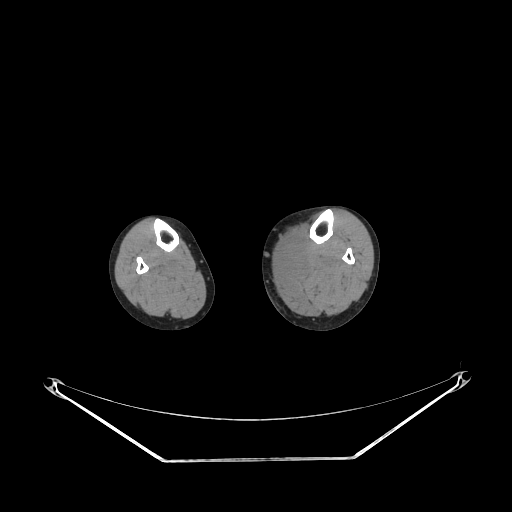
CT of an extremity soft-tissue mass (from a PET/CT study), one axial slice. Position 130 of 223 along the scan axis. Reconstruction kernel STANDARD. Soft-tissue window (W 400 / L 40 HU). 512 × 512 image matrix, field of view 500 × 500 mm. Female patient. From the clinical record (not read from this slice): histological type: extraskeletal high grade osteogenic sarcoma; grade: high; site of the primary tumour: left calf.
Structures marked on this image (expert contour drawn on MRI and transferred to this co-registered scan by the dataset authors):
- gross tumour volume (mass): box from (x=283, y=249) to (x=303, y=266) px